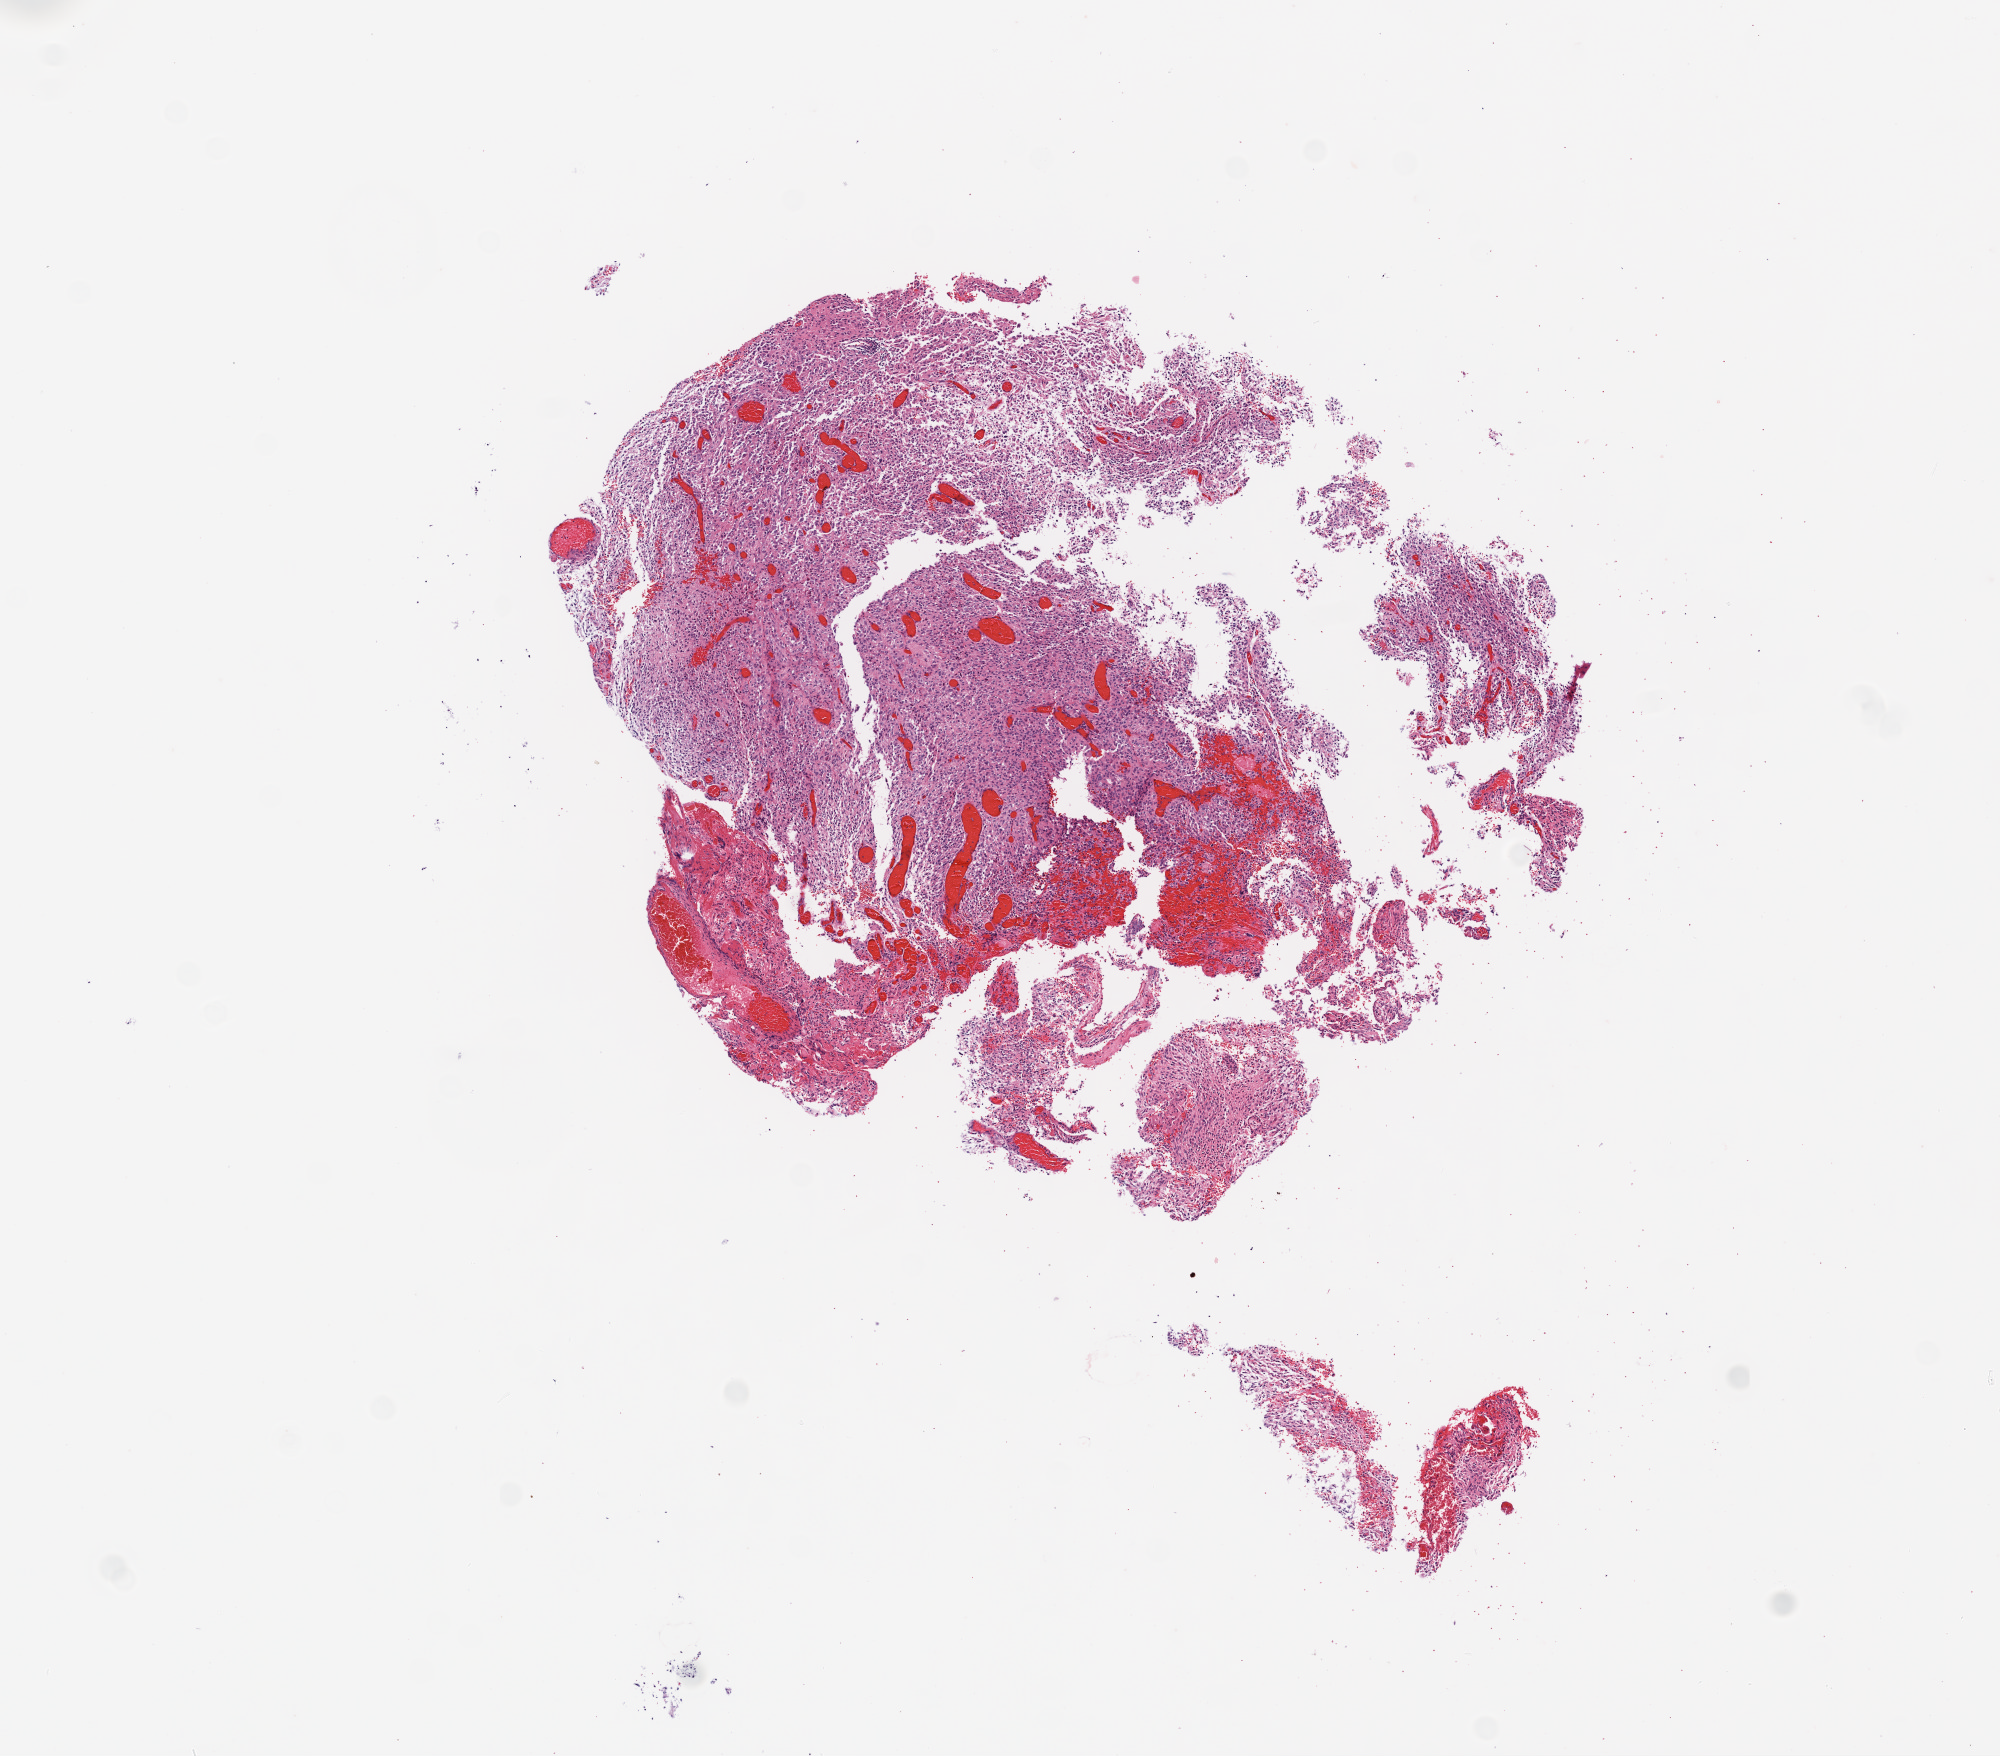
Whole-slide histology image, Hematoxylin and eosin (H&E) stained, a low-resolution overview of the entire scanned area, about 8.0 x 7.0 mm; formalin-fixed paraffin-embedded (FFPE) diagnostic section; brain, primary tumour sample. Male, age 54 years at initial diagnosis.
Pathologic diagnosis: Glioblastoma.